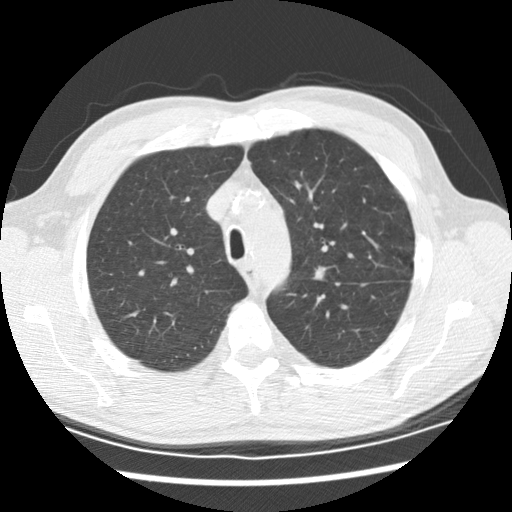
Low-dose screening chest CT, one axial slice. Slice 154 of 208 in the series (ordered by position). Reconstruction kernel STANDARD. 120 kVp. Lung window (W 1500 / L -600 HU). 2.5 mm slice thickness. 512 × 512 image matrix.
Structures marked on this image (manually delineated by an expert):
- lesion 1 (tumor, upper lobe of left lung): bounding box (x1, y1, x2, y2) in pixels: (313, 266, 326, 281)